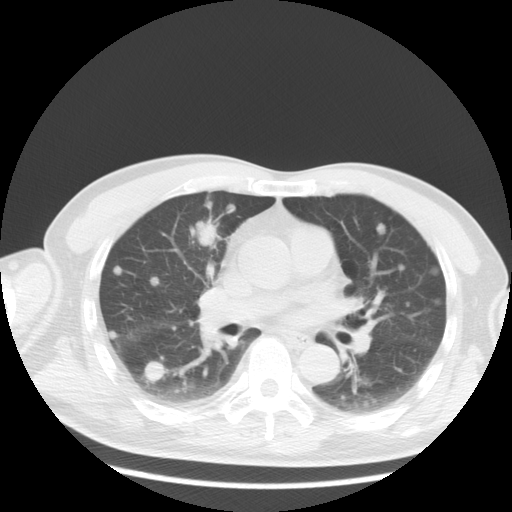
Chest CT, one axial slice. Reconstruction kernel STANDARD. Lung window (W 1500 / L -600 HU). 512 × 512 image matrix, field of view 369 × 369 mm. Patient: male, 57 years. Case-level facts recorded for this patient, not image findings: clinical TNM (as recorded): T2 N3 M1a.
Outlined on this slice (rectangle marked by the reading radiologist):
- lung tumour (recorded histology: adenocarcinoma): bounding box (x1, y1, x2, y2) in pixels: (199, 221, 216, 248)